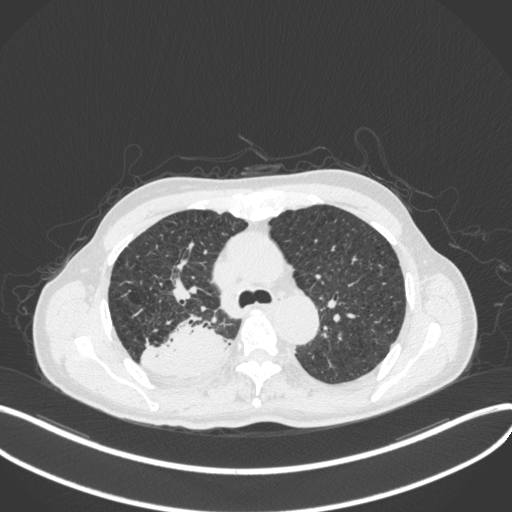
Chest CT, one axial slice; slice 312 of 423 in the series (ordered by position); reconstruction kernel B31f; lung window (W 1500 / L -600 HU); 512 × 512 image matrix, field of view 400 × 400 mm. Patient: male, 79 years. Case-level facts recorded for this patient, not image findings: clinical TNM (as recorded): T3 N0 M0.
Structures marked on this image (bounding box drawn by a radiologist):
- lung tumour (recorded histology: adenocarcinoma): box from (x=137, y=314) to (x=229, y=379) px